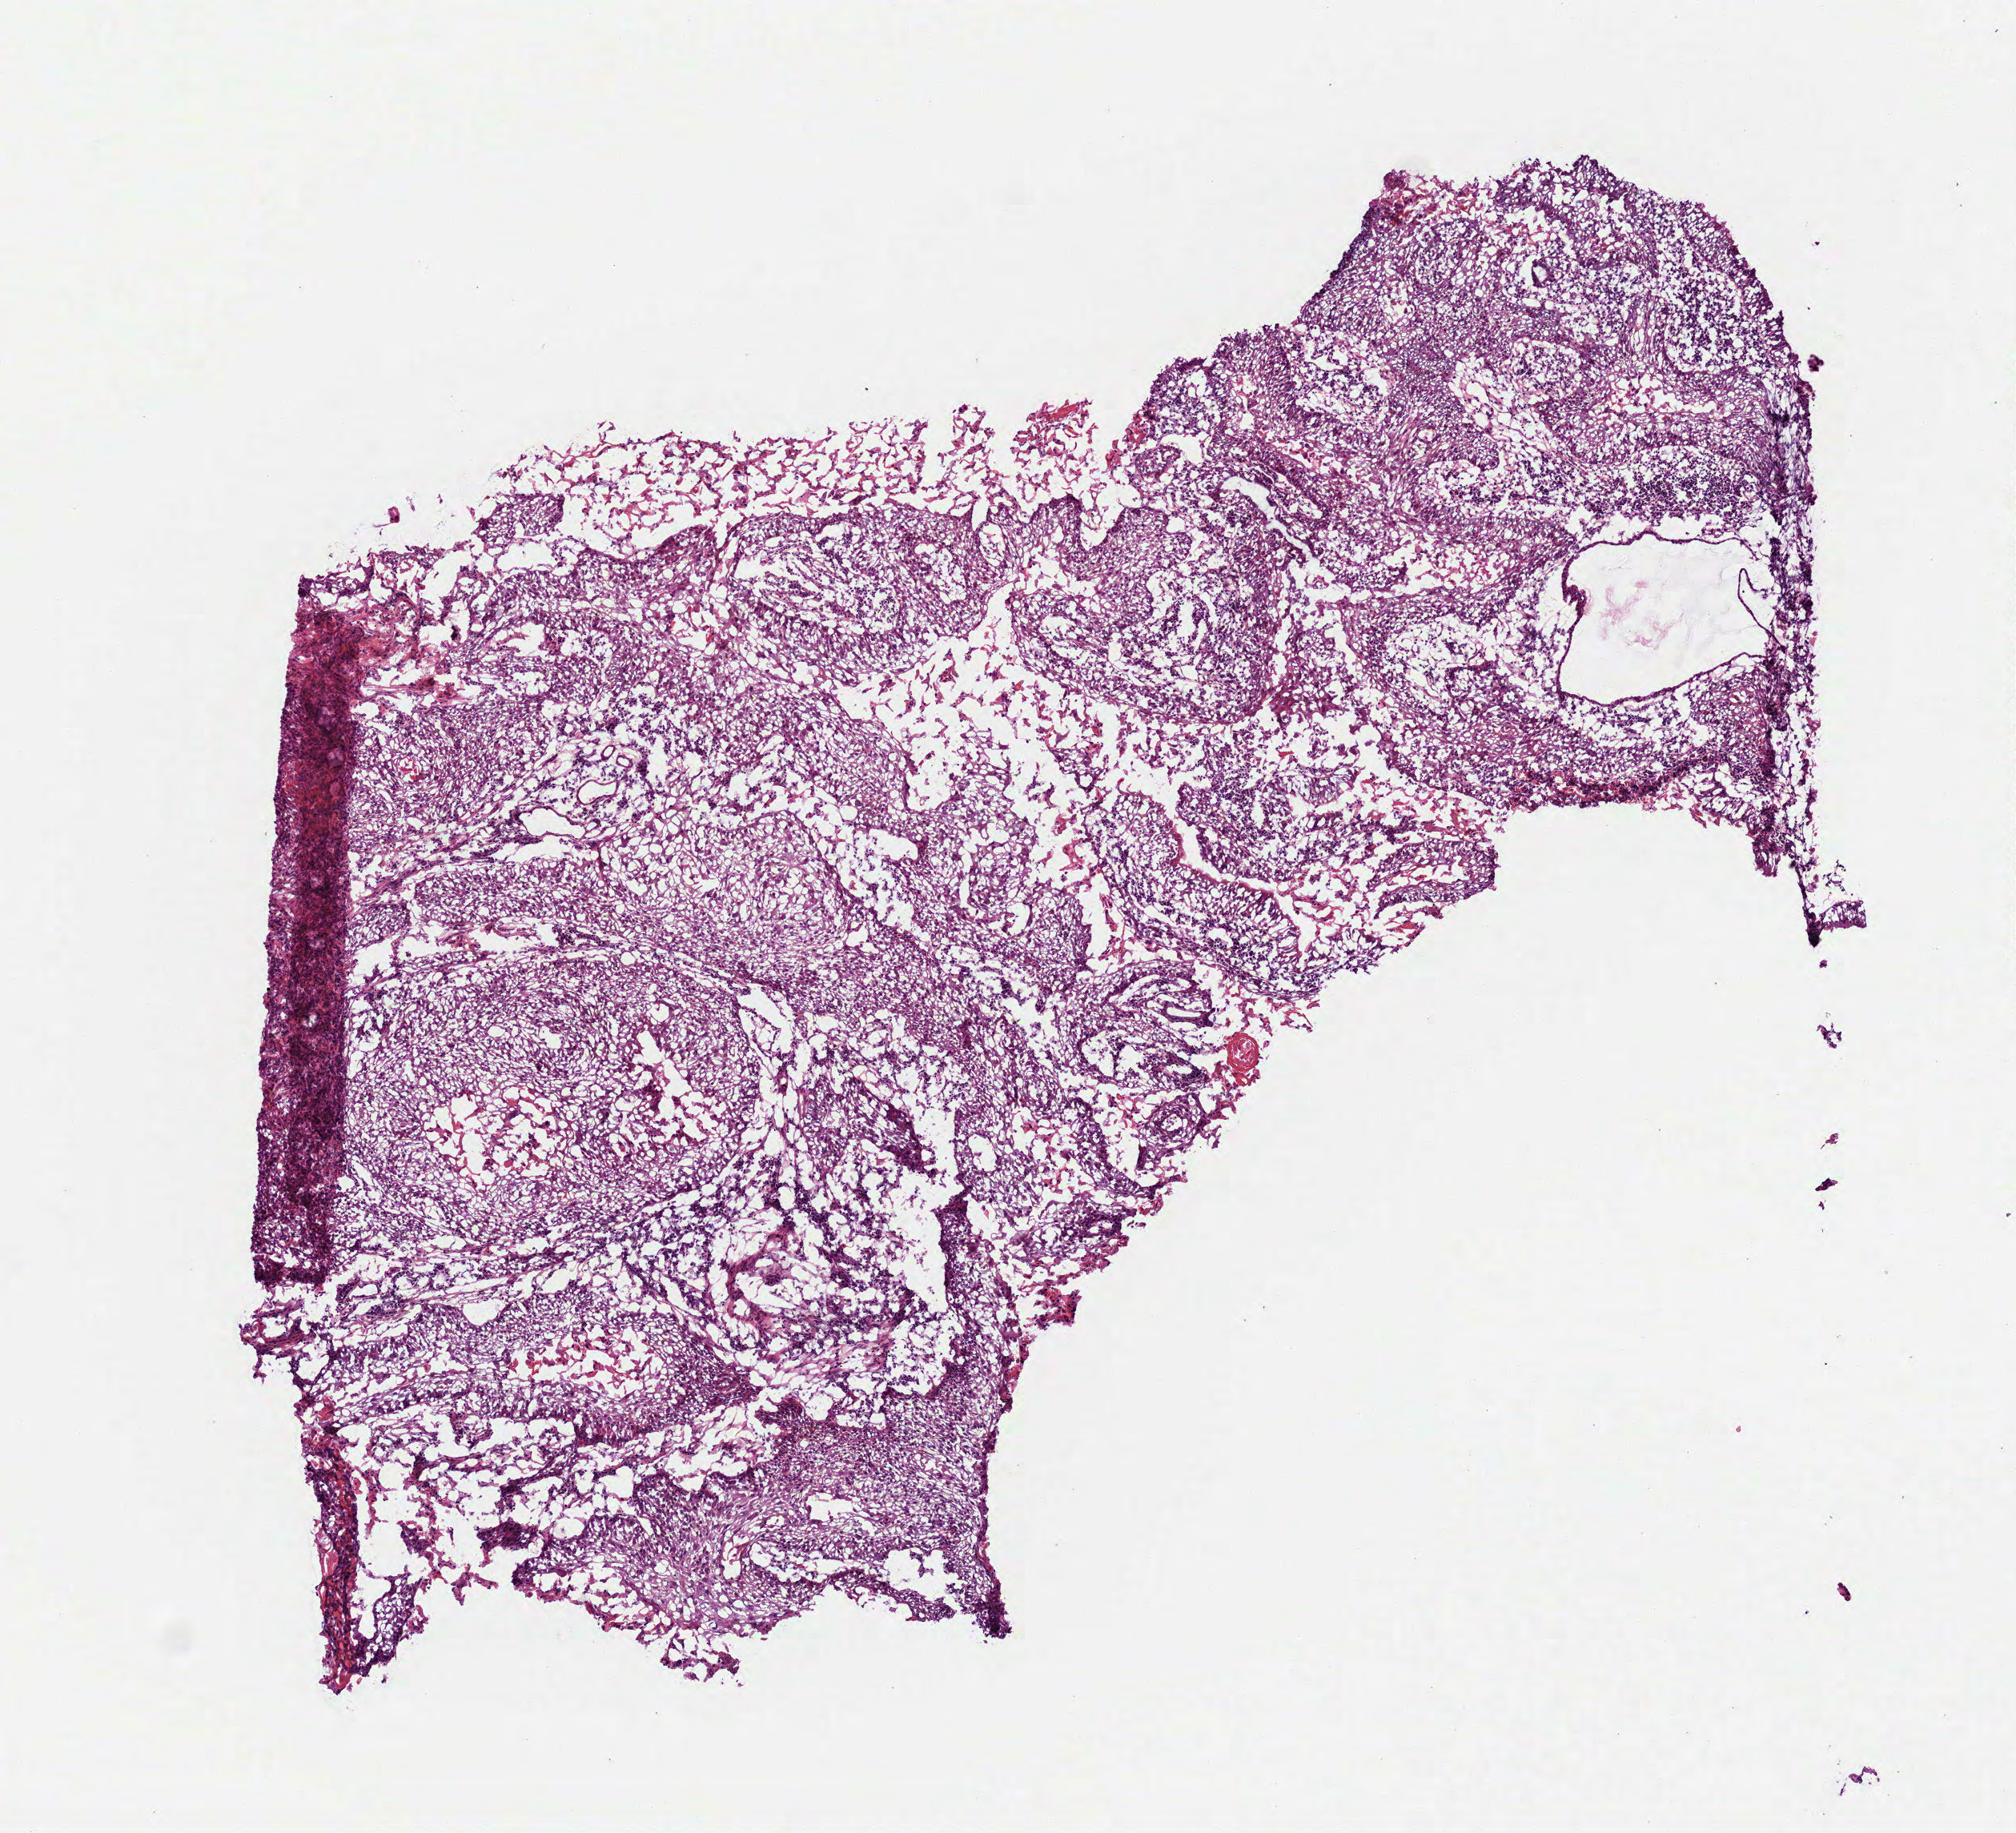
Digitized H&E-stained tissue section (whole slide) — low-resolution overview of the scanned area, about 5.1 x 4.6 mm (slide scanned at 40x), frozen section, sample: primary tumour, head and neck. Female patient; age at initial diagnosis 60 years. Histologic grade: G2 (moderately differentiated). Slide review estimates, as recorded: tumour cells 90%, tumour nuclei 80%, normal cells 0%, stromal cells 10%, necrosis 0%.
AJCC pathologic stage: II (7th edition). Pathologic diagnosis: Squamous cell carcinoma, NOS (larynx, NOS).